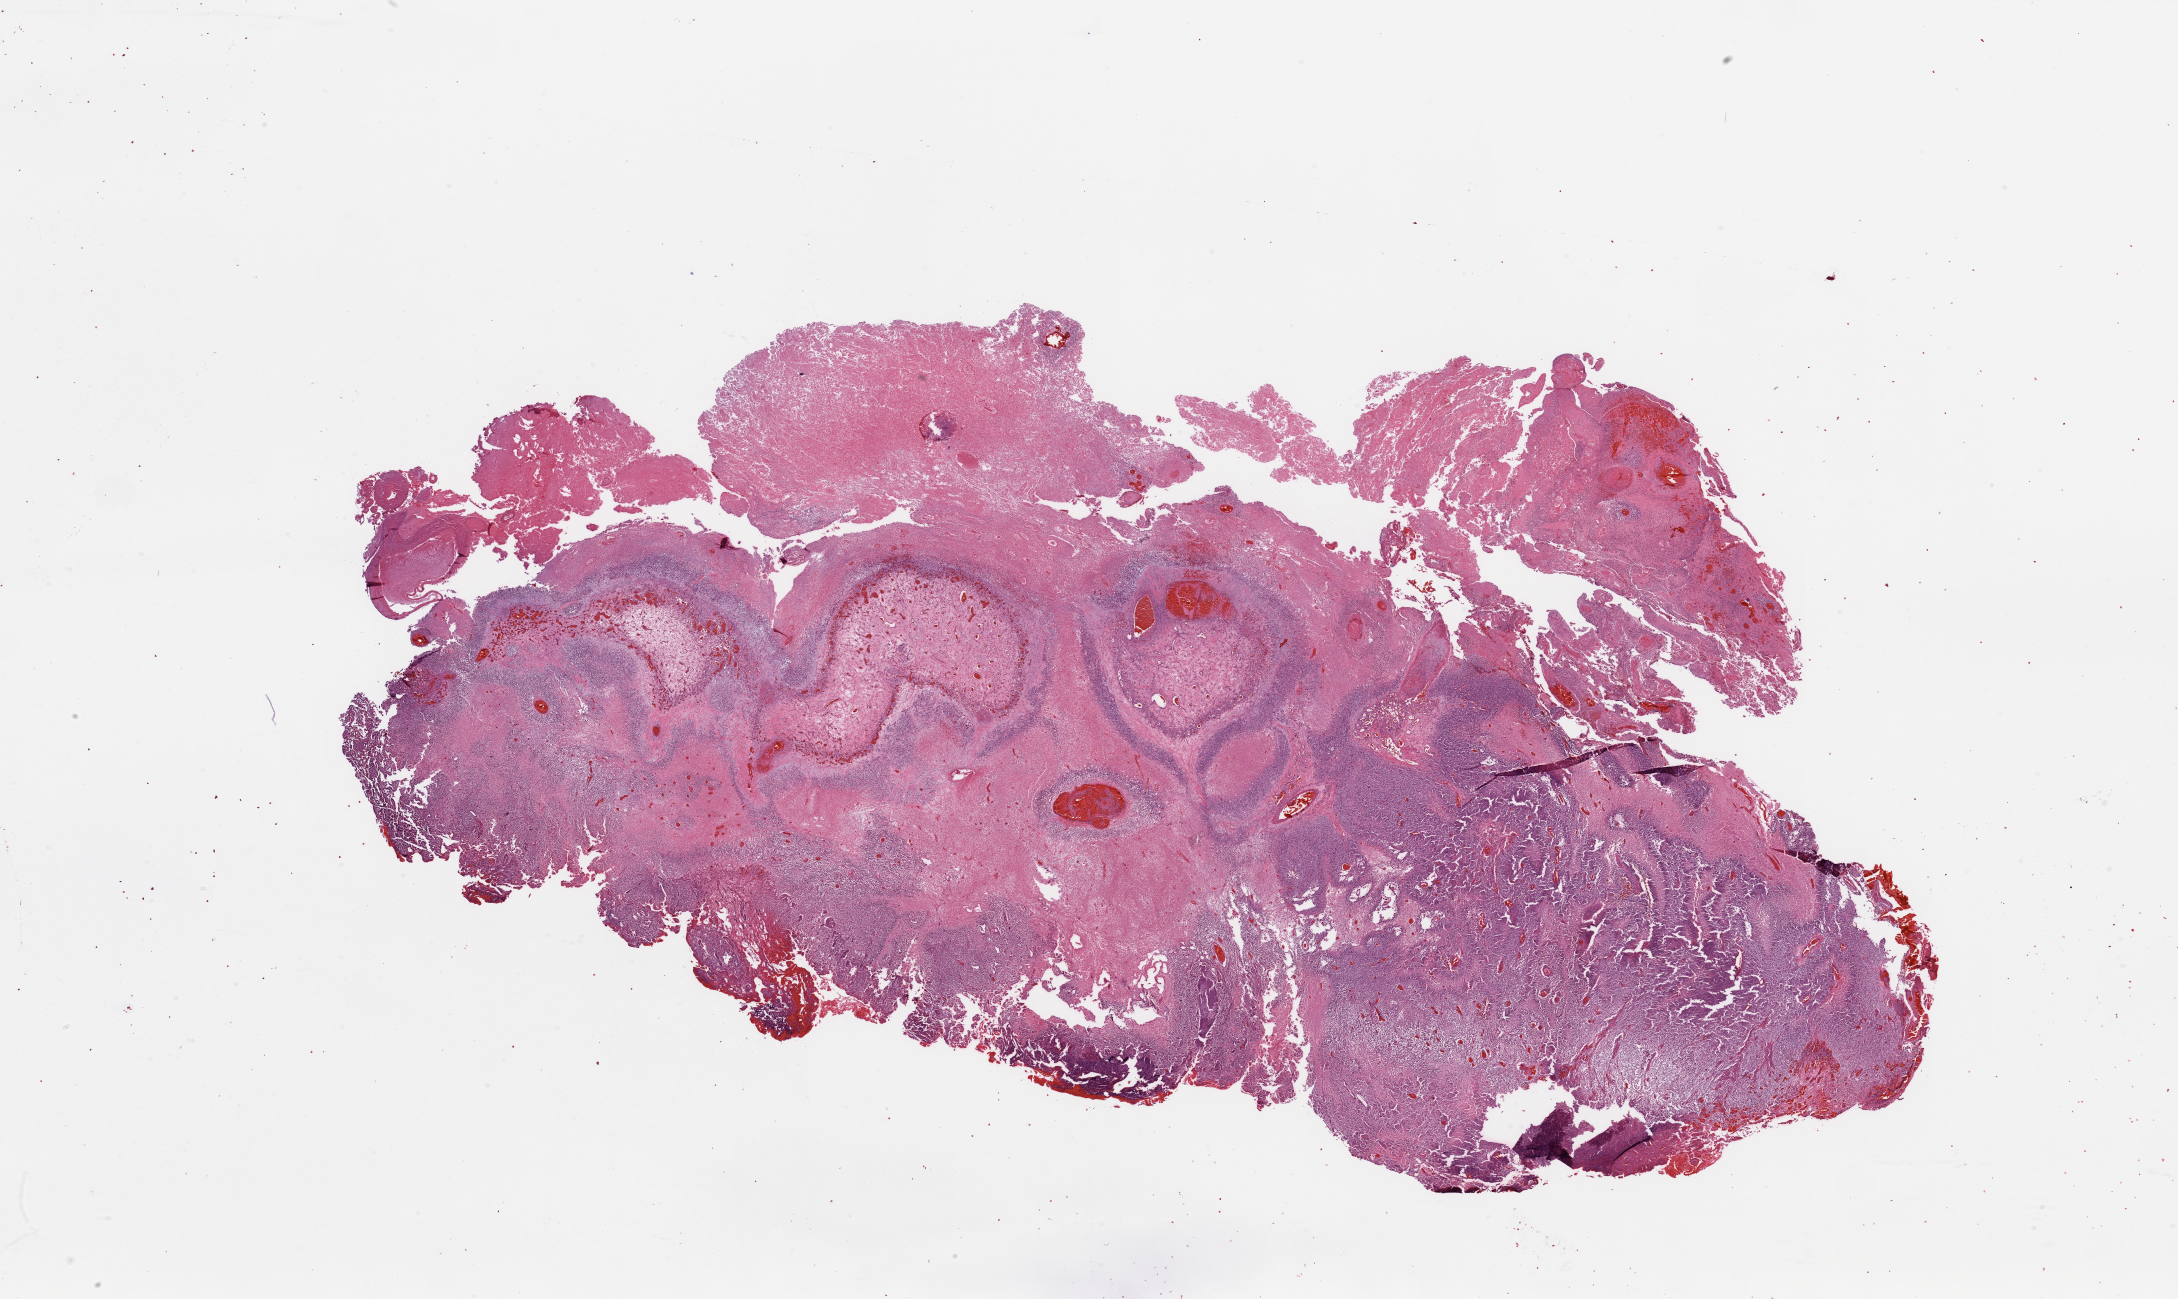
Whole-slide histology image, H&E, a low-resolution overview of the entire scanned area, about 34.5 x 20.5 mm (from a 20x scan); tumour tissue sample, brain. Patient: male, age 62 years.
- patient diagnosis (cohort enrolment): glioblastoma multiforme (brain)
- primary tumour site (as recorded): frontal lobe